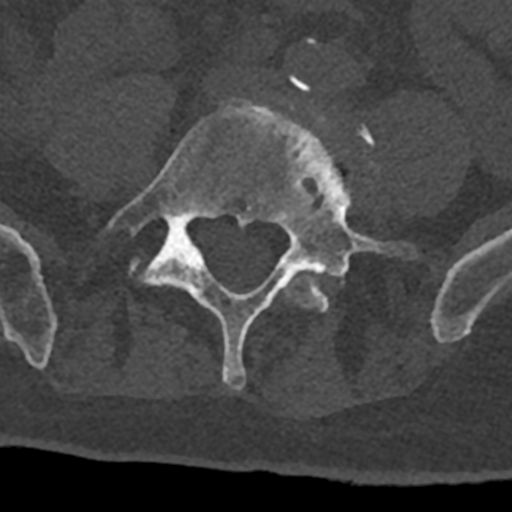
CT including the spine, one axial slice. Slice 209 of 797 in the series (ordered by position). 120 kVp. Bone window (W 1800 / L 400 HU). 512 × 512 image matrix, field of view 160 × 160 mm. Male patient, age 74 years. Case-level facts recorded for this patient, not image findings: primary cancer: renal; vertebrae with lytic lesions (as recorded): T10, L1, L2, L3, L4, L5.
Outlined on this slice (semi-automatic segmentation, software-assisted and operator-edited):
- L4 vertebra: box from (x=283, y=81) to (x=375, y=312) px
- L5 vertebra: (x=108, y=99)–(x=411, y=390)